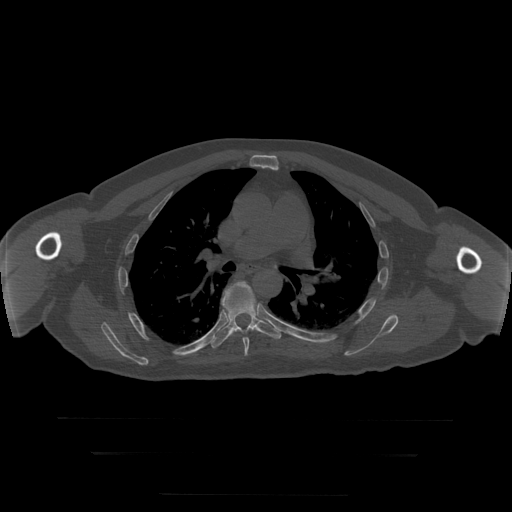
CT including the spine, one axial slice; slice 195 of 397 in the series (ordered by position); reconstruction kernel STANDARD; bone window (W 1800 / L 400 HU); 1.25 mm slice thickness; 512 × 512 image matrix. Patient age 73 years. From the clinical record (not read from this slice): primary cancer: prostate.
Annotated regions visible in this slice (semi-automatic segmentation, software-assisted and operator-edited):
- T6 vertebra: bounding box <223,297,257,356> (left, top, right, bottom; pixels)
- T7 vertebra: <210,282,282,349>